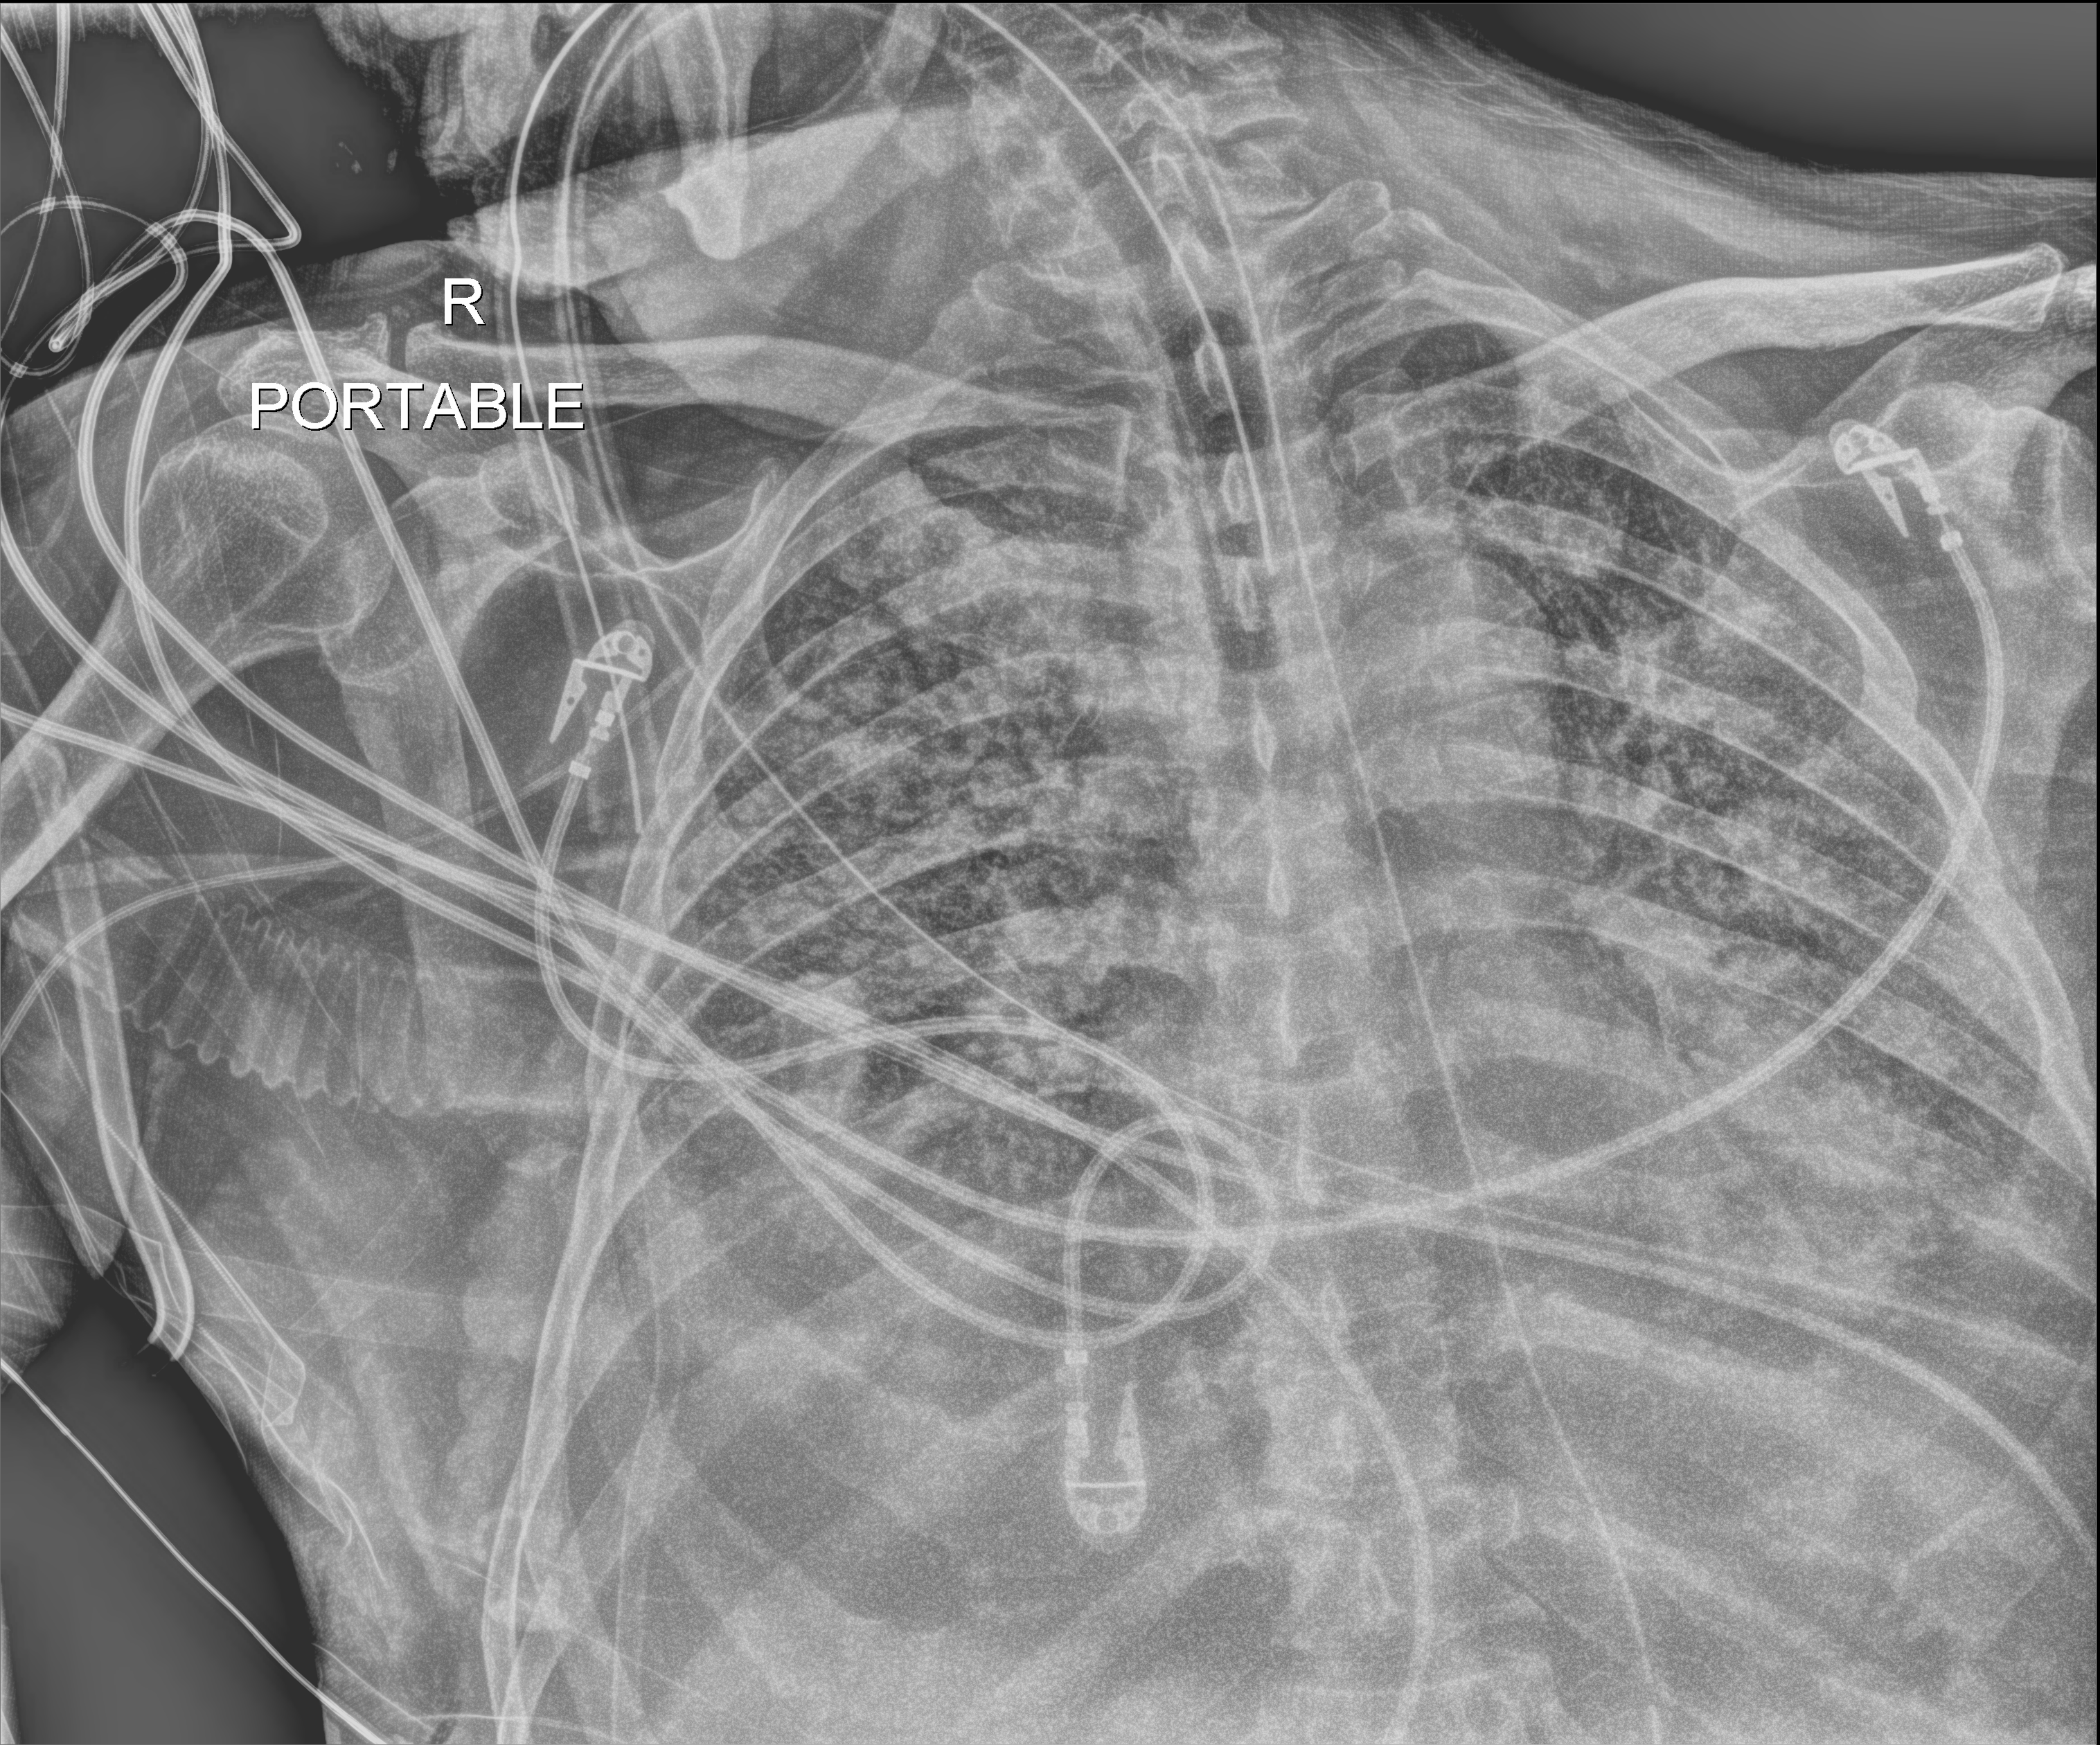
Chest X-ray (portable), anteroposterior (AP) projection. Patient hospitalised with COVID-19; male, aged 60–74 years.
Hospital-stay facts (about this admission, not read from this image; timing relative to this image not recorded): length of hospital stay: 26 days; mechanically ventilated during this hospital stay: yes; chronic kidney disease (admission record): no.